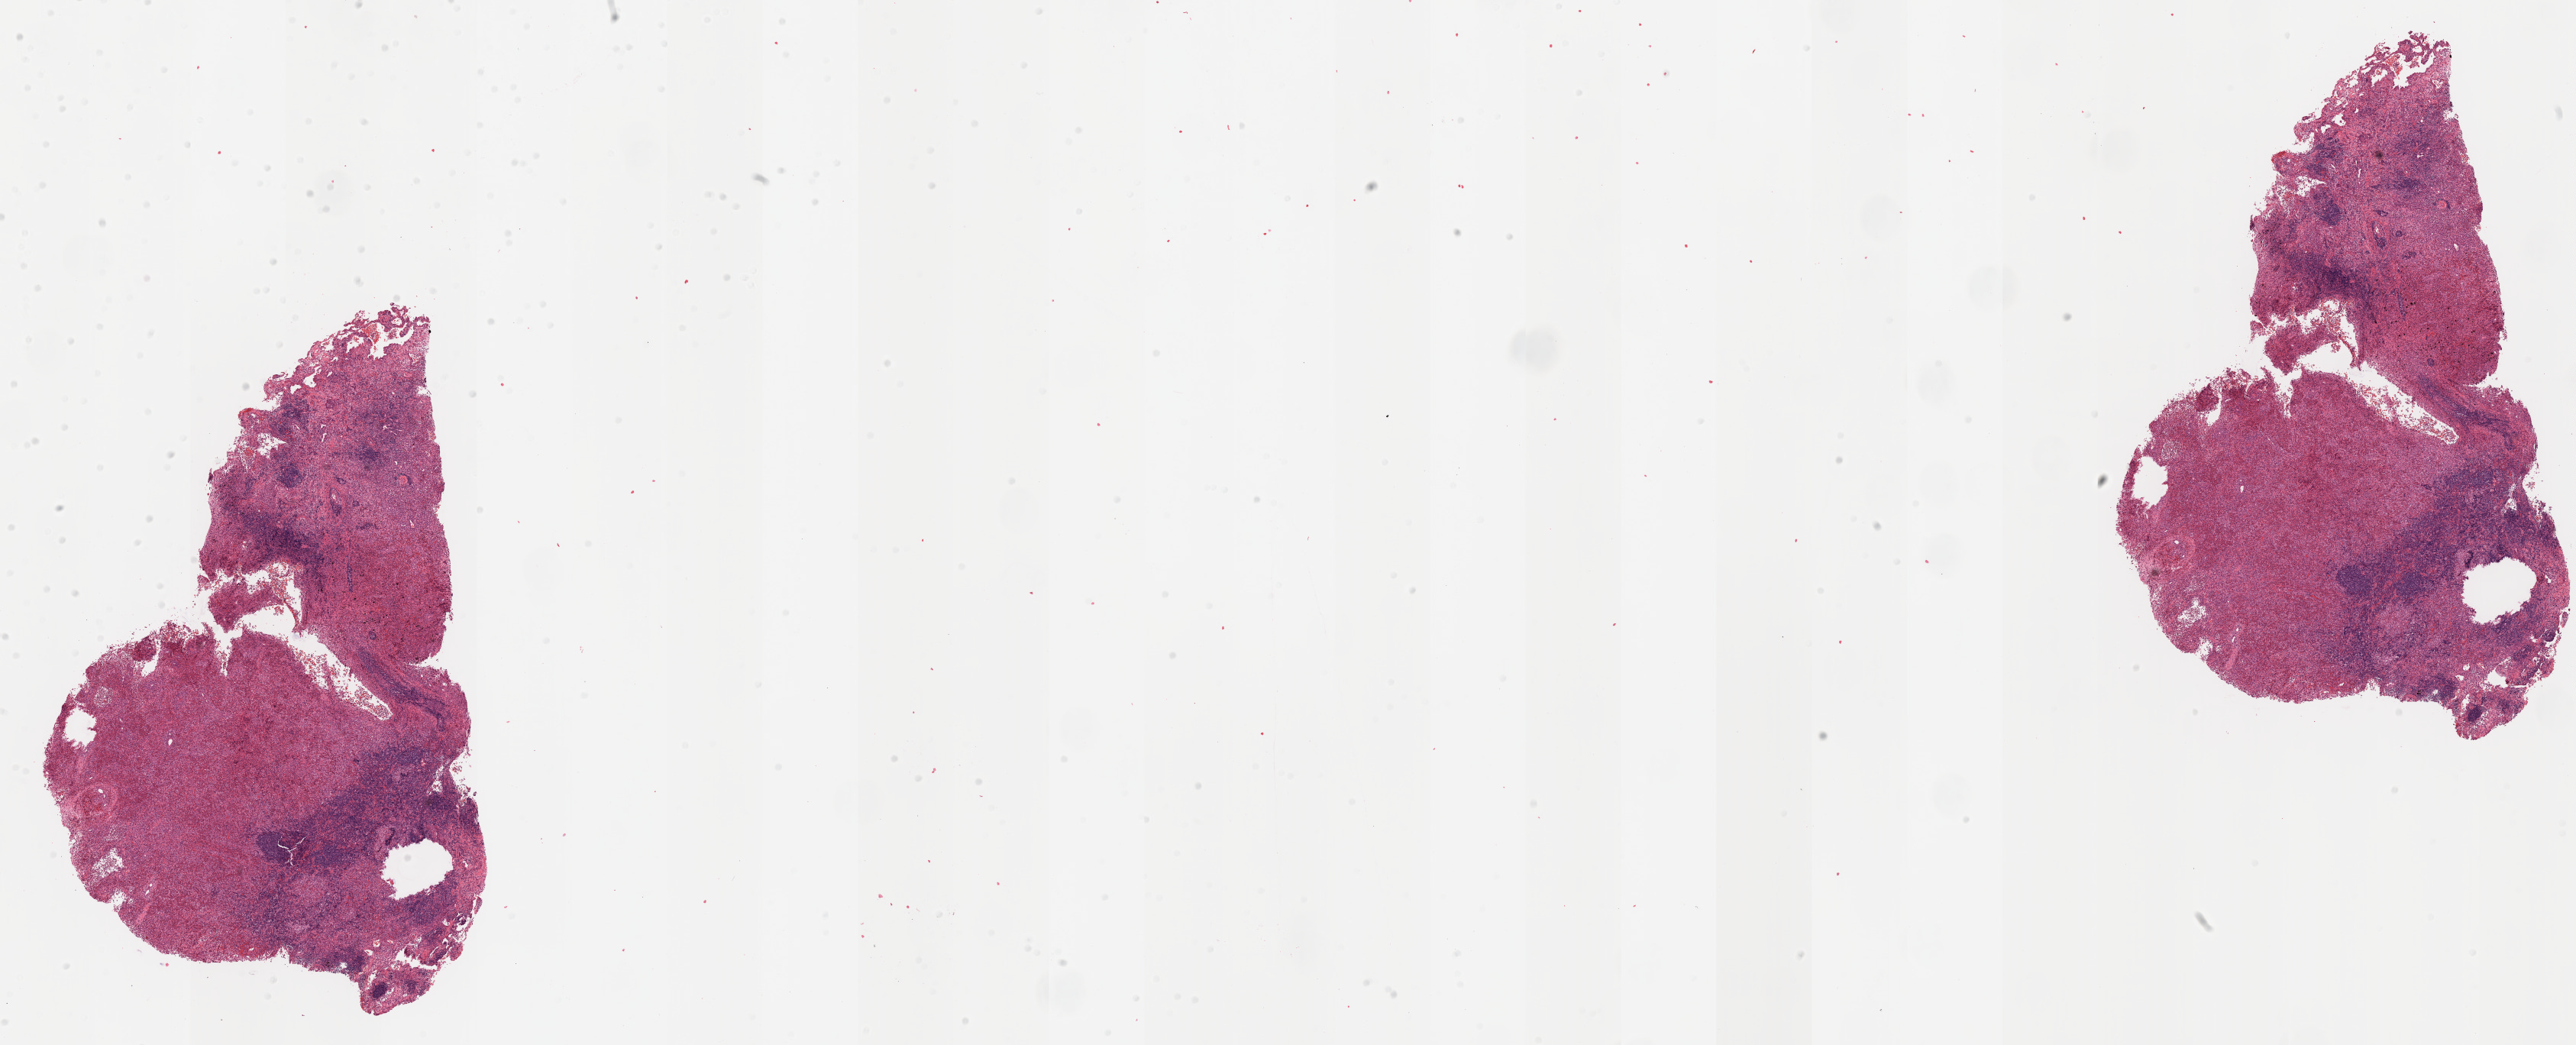
H&E-stained whole-slide image, a low-resolution overview of the entire scanned area, about 27.0 x 11.0 mm; formalin-fixed paraffin-embedded (FFPE) diagnostic section; lung, primary tumour sample. Male patient.
AJCC pathologic stage: IB. Pathologic diagnosis: Adenocarcinoma, NOS (upper lobe, lung).